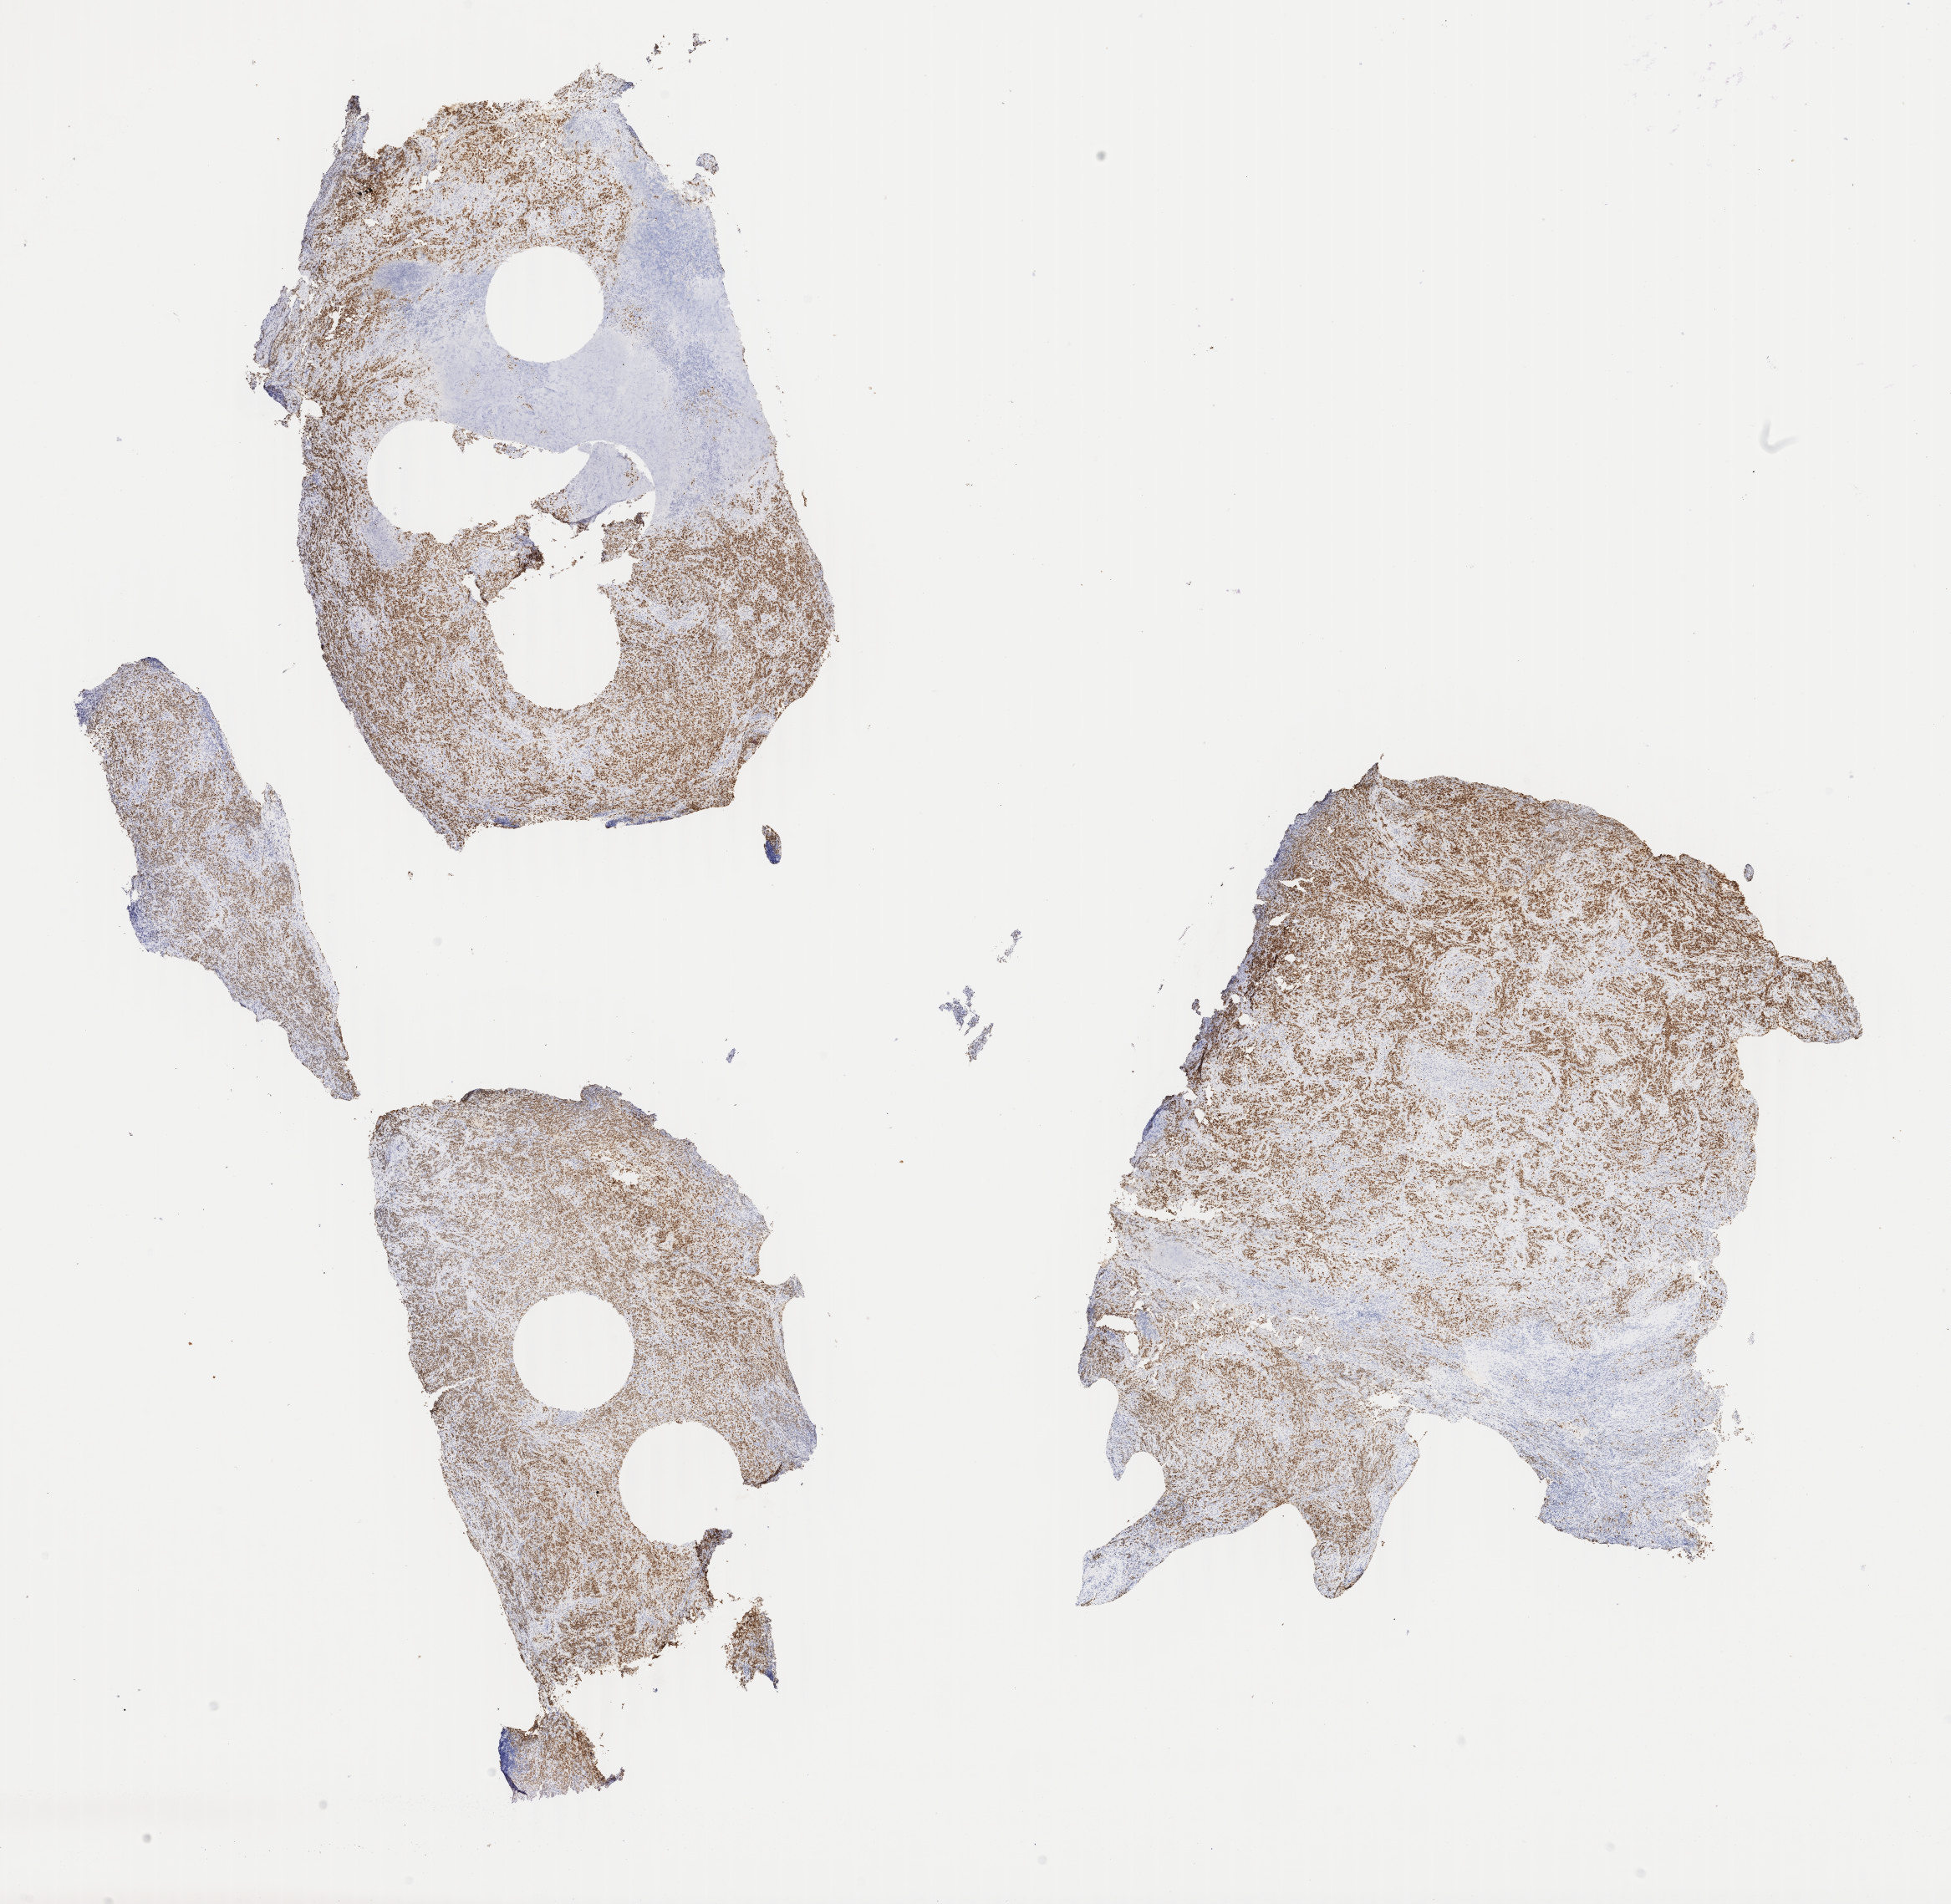
Immunohistochemistry (IHC) whole-slide image stained for TTF-1 (thyroid transcription factor 1), low-resolution overview of the scanned area, about 18.6 x 18.1 mm, specimen: tumor tissue, anatomic site: lung (left). Patient male; aged 65.
Diagnosis: Carcinoma, undifferentiated, NOS.